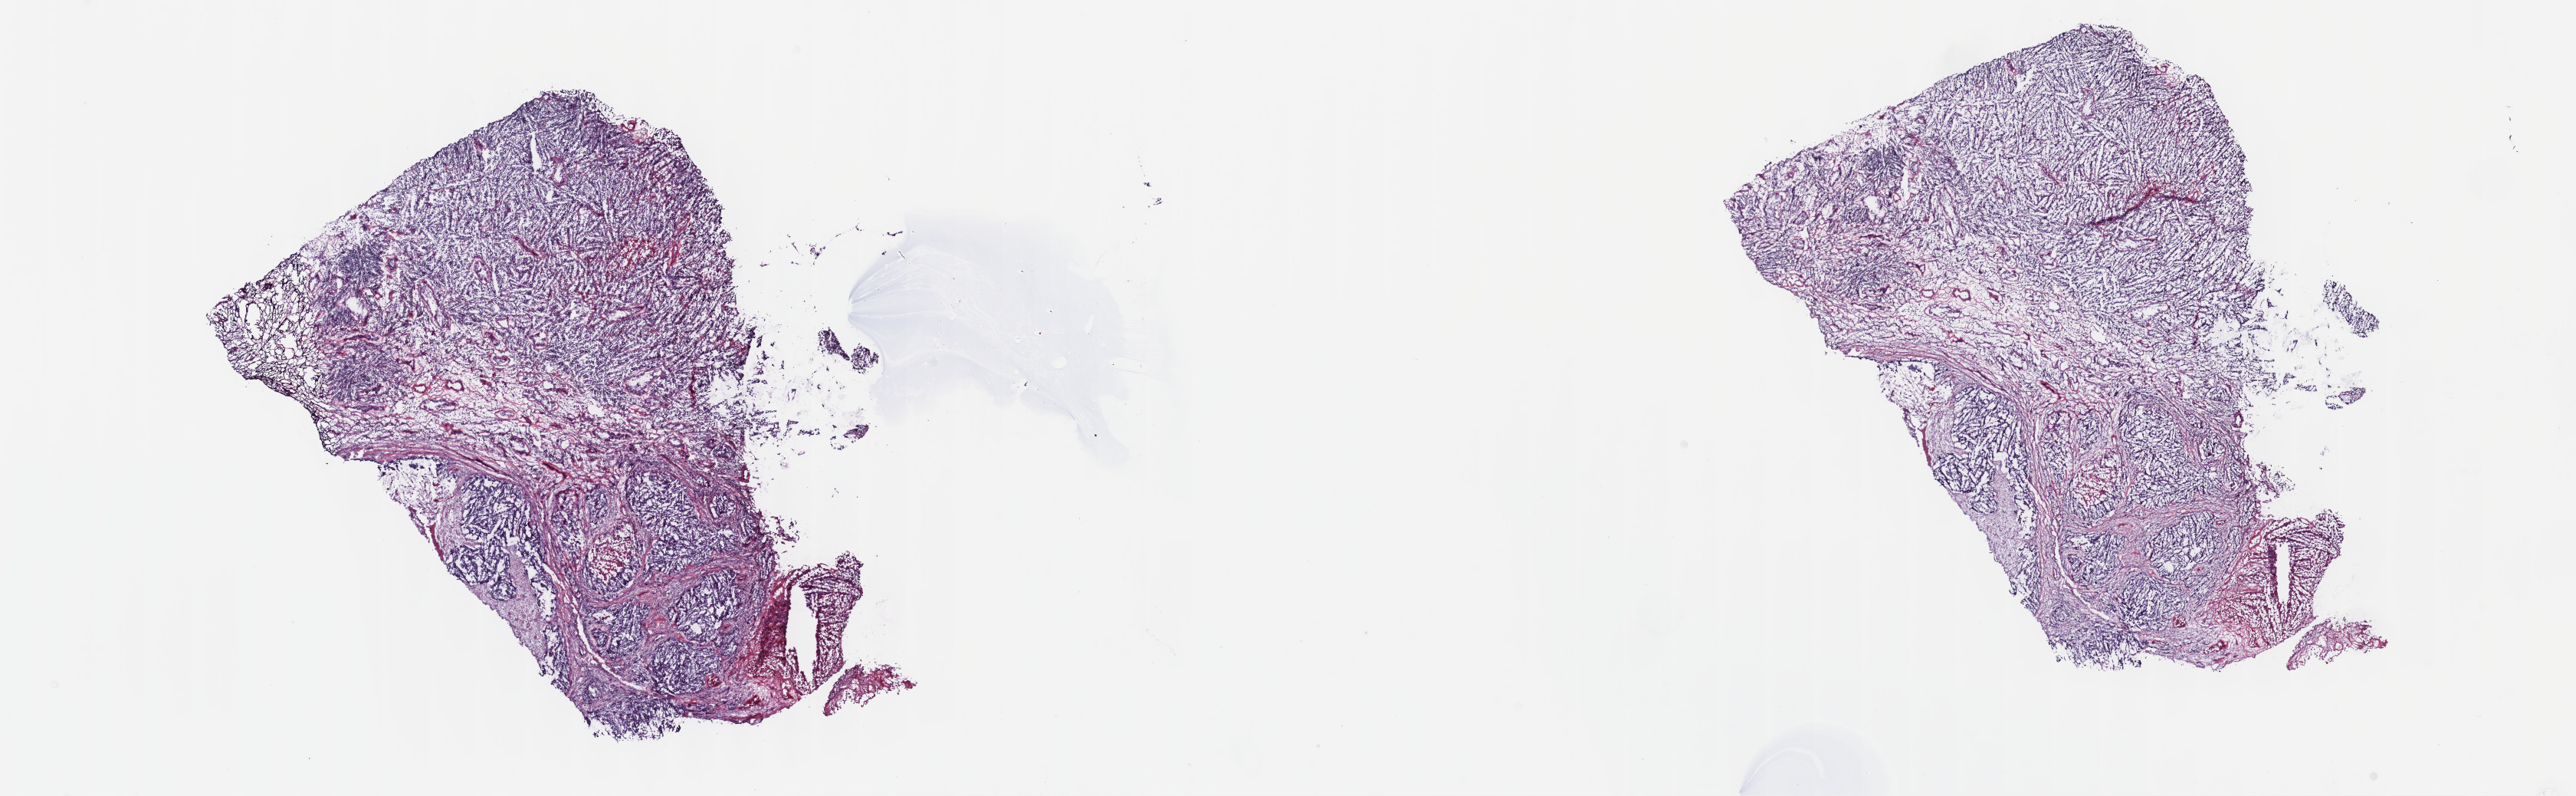
Digitized H&E tissue section (whole slide), a low-resolution overview of the entire scanned area, about 27.2 x 8.4 mm (slide scanned at 40x). Frozen section from the top of the tissue portion. Testis, primary tumour sample. Male patient; age at initial diagnosis 19 years. Slide review estimates, as recorded: tumour cells 100%, tumour nuclei 65%, normal cells 0%, stromal cells 0%, necrosis 0%. Inflammatory infiltration, as recorded: lymphocyte infiltration 3%, monocyte infiltration 0%, neutrophil infiltration 0%.
Laterality: right. AJCC pathologic stage: II (4th edition). Histologic diagnosis: Embryonal carcinoma, NOS.